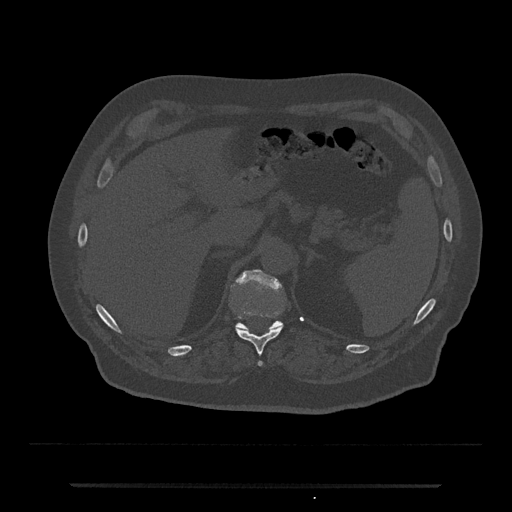
CT including the spine, one axial slice; position 632 of 797 along the scan axis; reconstruction kernel Br40s/3; 120 kVp; bone window (W 1800 / L 400 HU); 512 × 512 image matrix. Male patient, age 80 years. From the clinical record (not read from this slice): primary cancer: prostate; vertebrae with lytic lesions (as recorded): L1, T11.
Outlined on this slice (semi-automatically segmented with operator editing):
- T11 vertebra: bounding box (x1, y1, x2, y2) in pixels: (236, 326, 282, 366)
- T12 vertebra: (235, 269, 282, 331)